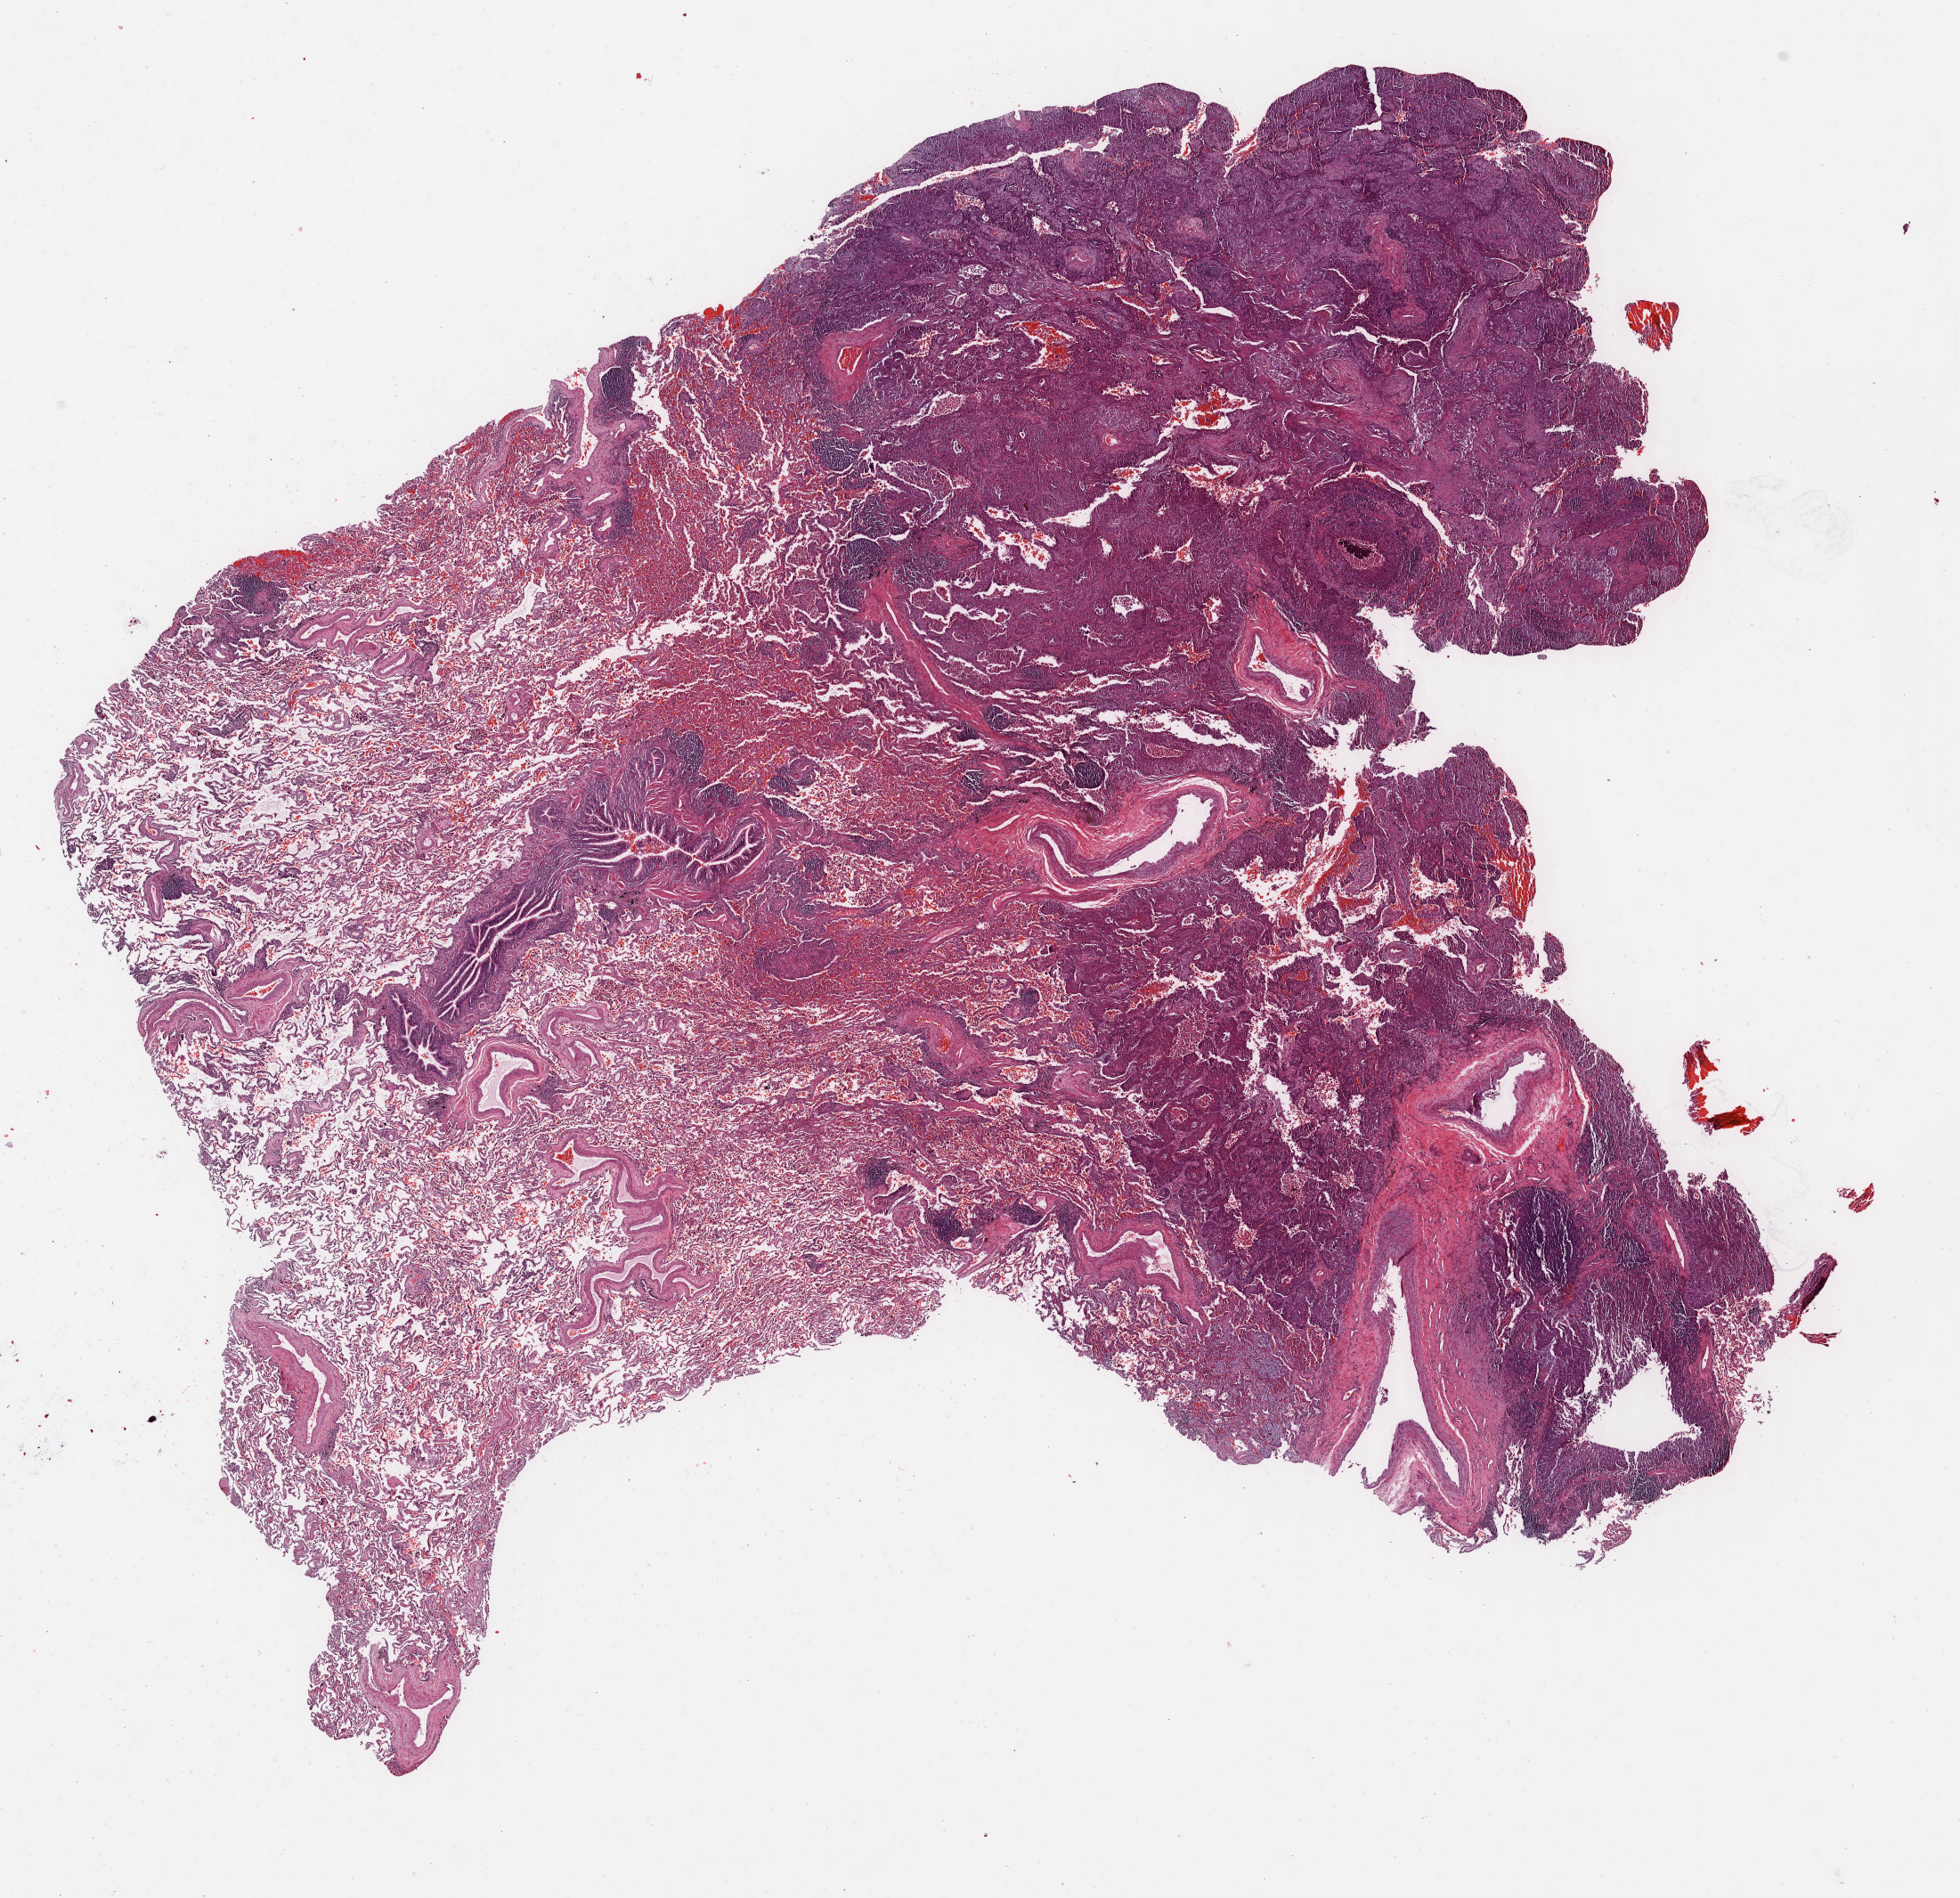
H&E whole-slide image — a low-resolution overview of the entire scanned area, about 17.3 x 16.8 mm; FFPE section; sample: primary tumour, lung. Male, age 73 years at initial diagnosis.
Laterality: right. TNM: T1 N0 MX. AJCC pathologic stage: IA. Pathologic diagnosis: Squamous cell carcinoma, NOS (lower lobe, lung).